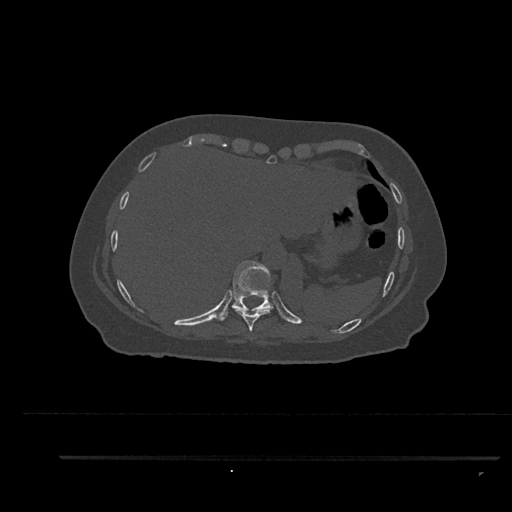
CT including the spine, one axial slice. Position 391 of 797 along the scan axis. Reconstruction kernel Br40s/3. Bone window (W 1800 / L 400 HU). 0.5 mm slice thickness. 512 × 512 image matrix, field of view 408 × 408 mm. Patient: female, 44 years. From the clinical record (not read from this slice): primary cancer: renal; vertebrae with lytic lesions (as recorded): L1.
Outlined on this slice (semi-automatically segmented with operator editing):
- T10 vertebra: bounding box (x1, y1, x2, y2) in pixels: (217, 260, 274, 321)
- T9 vertebra: (235, 308, 273, 331)